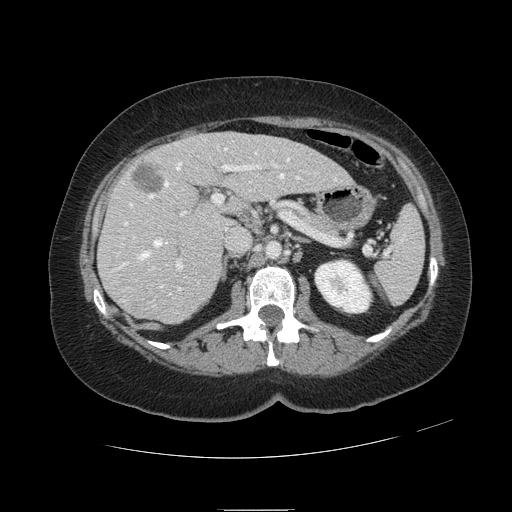
Contrast-enhanced abdominal CT, one axial slice. Position 60 of 121 along the scan axis. Soft-tissue window (W 400 / L 40 HU). 2.5 mm slice thickness. 512 × 512 image matrix, field of view 400 × 400 mm. Female patient, age 52 years. From the clinical record (not read from this slice): diagnosis: colorectal cancer liver metastases, imaged before liver resection; multiple liver metastases: yes; largest metastasis: 6.3 cm; disease in both lobes: no.
Outlined on this slice (expert manual segmentation):
- hepatic veins: bounding box <118,148,336,295> (left, top, right, bottom; pixels)
- liver: <99,133,351,323>
- planned liver remnant (the part of the liver to remain after resection): <168,132,351,204>
- portal vein (with intrahepatic branches): <124,164,278,270>
- liver metastasis: <132,164,164,194>